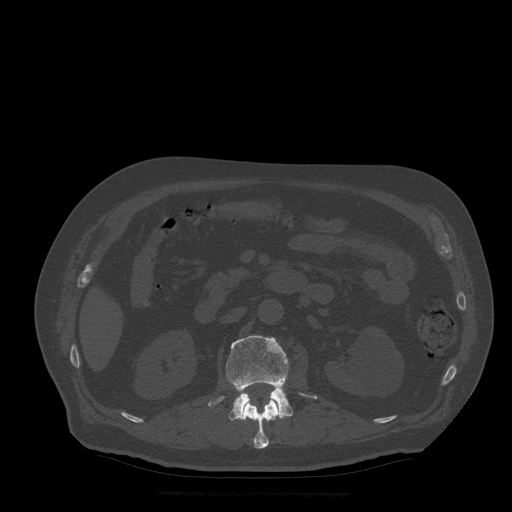
CT including the spine, one axial slice. Slice 179 of 522 in the series (ordered by position). Bone window (W 1800 / L 400 HU). 1.25 mm slice thickness. 512 × 512 image matrix, field of view 420 × 420 mm. Patient age 72 years. From the clinical record (not read from this slice): primary cancer: prostate.
Structures marked on this image (semi-automatically segmented with operator editing):
- L1 vertebra: box from (x=242, y=398) to (x=280, y=449) px
- L2 vertebra: (x=208, y=336)–(x=317, y=421)